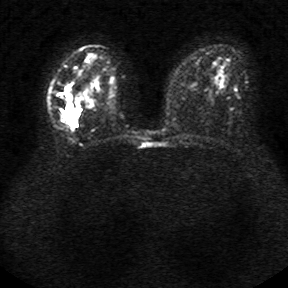
Breast MRI, one axial slice; position 18 of 34 along the scan axis; diffusion-weighted series; image 2 of 4 stored at this slice position (different b-values; order by instance number); 1.5 T; 5 mm slice thickness; 288 × 288 image matrix, field of view 340 × 340 mm. Female patient.
Annotated regions visible in this slice (outlined manually by an expert reader):
- tumour on diffusion-weighted imaging: box from (x=65, y=84) to (x=81, y=127) px